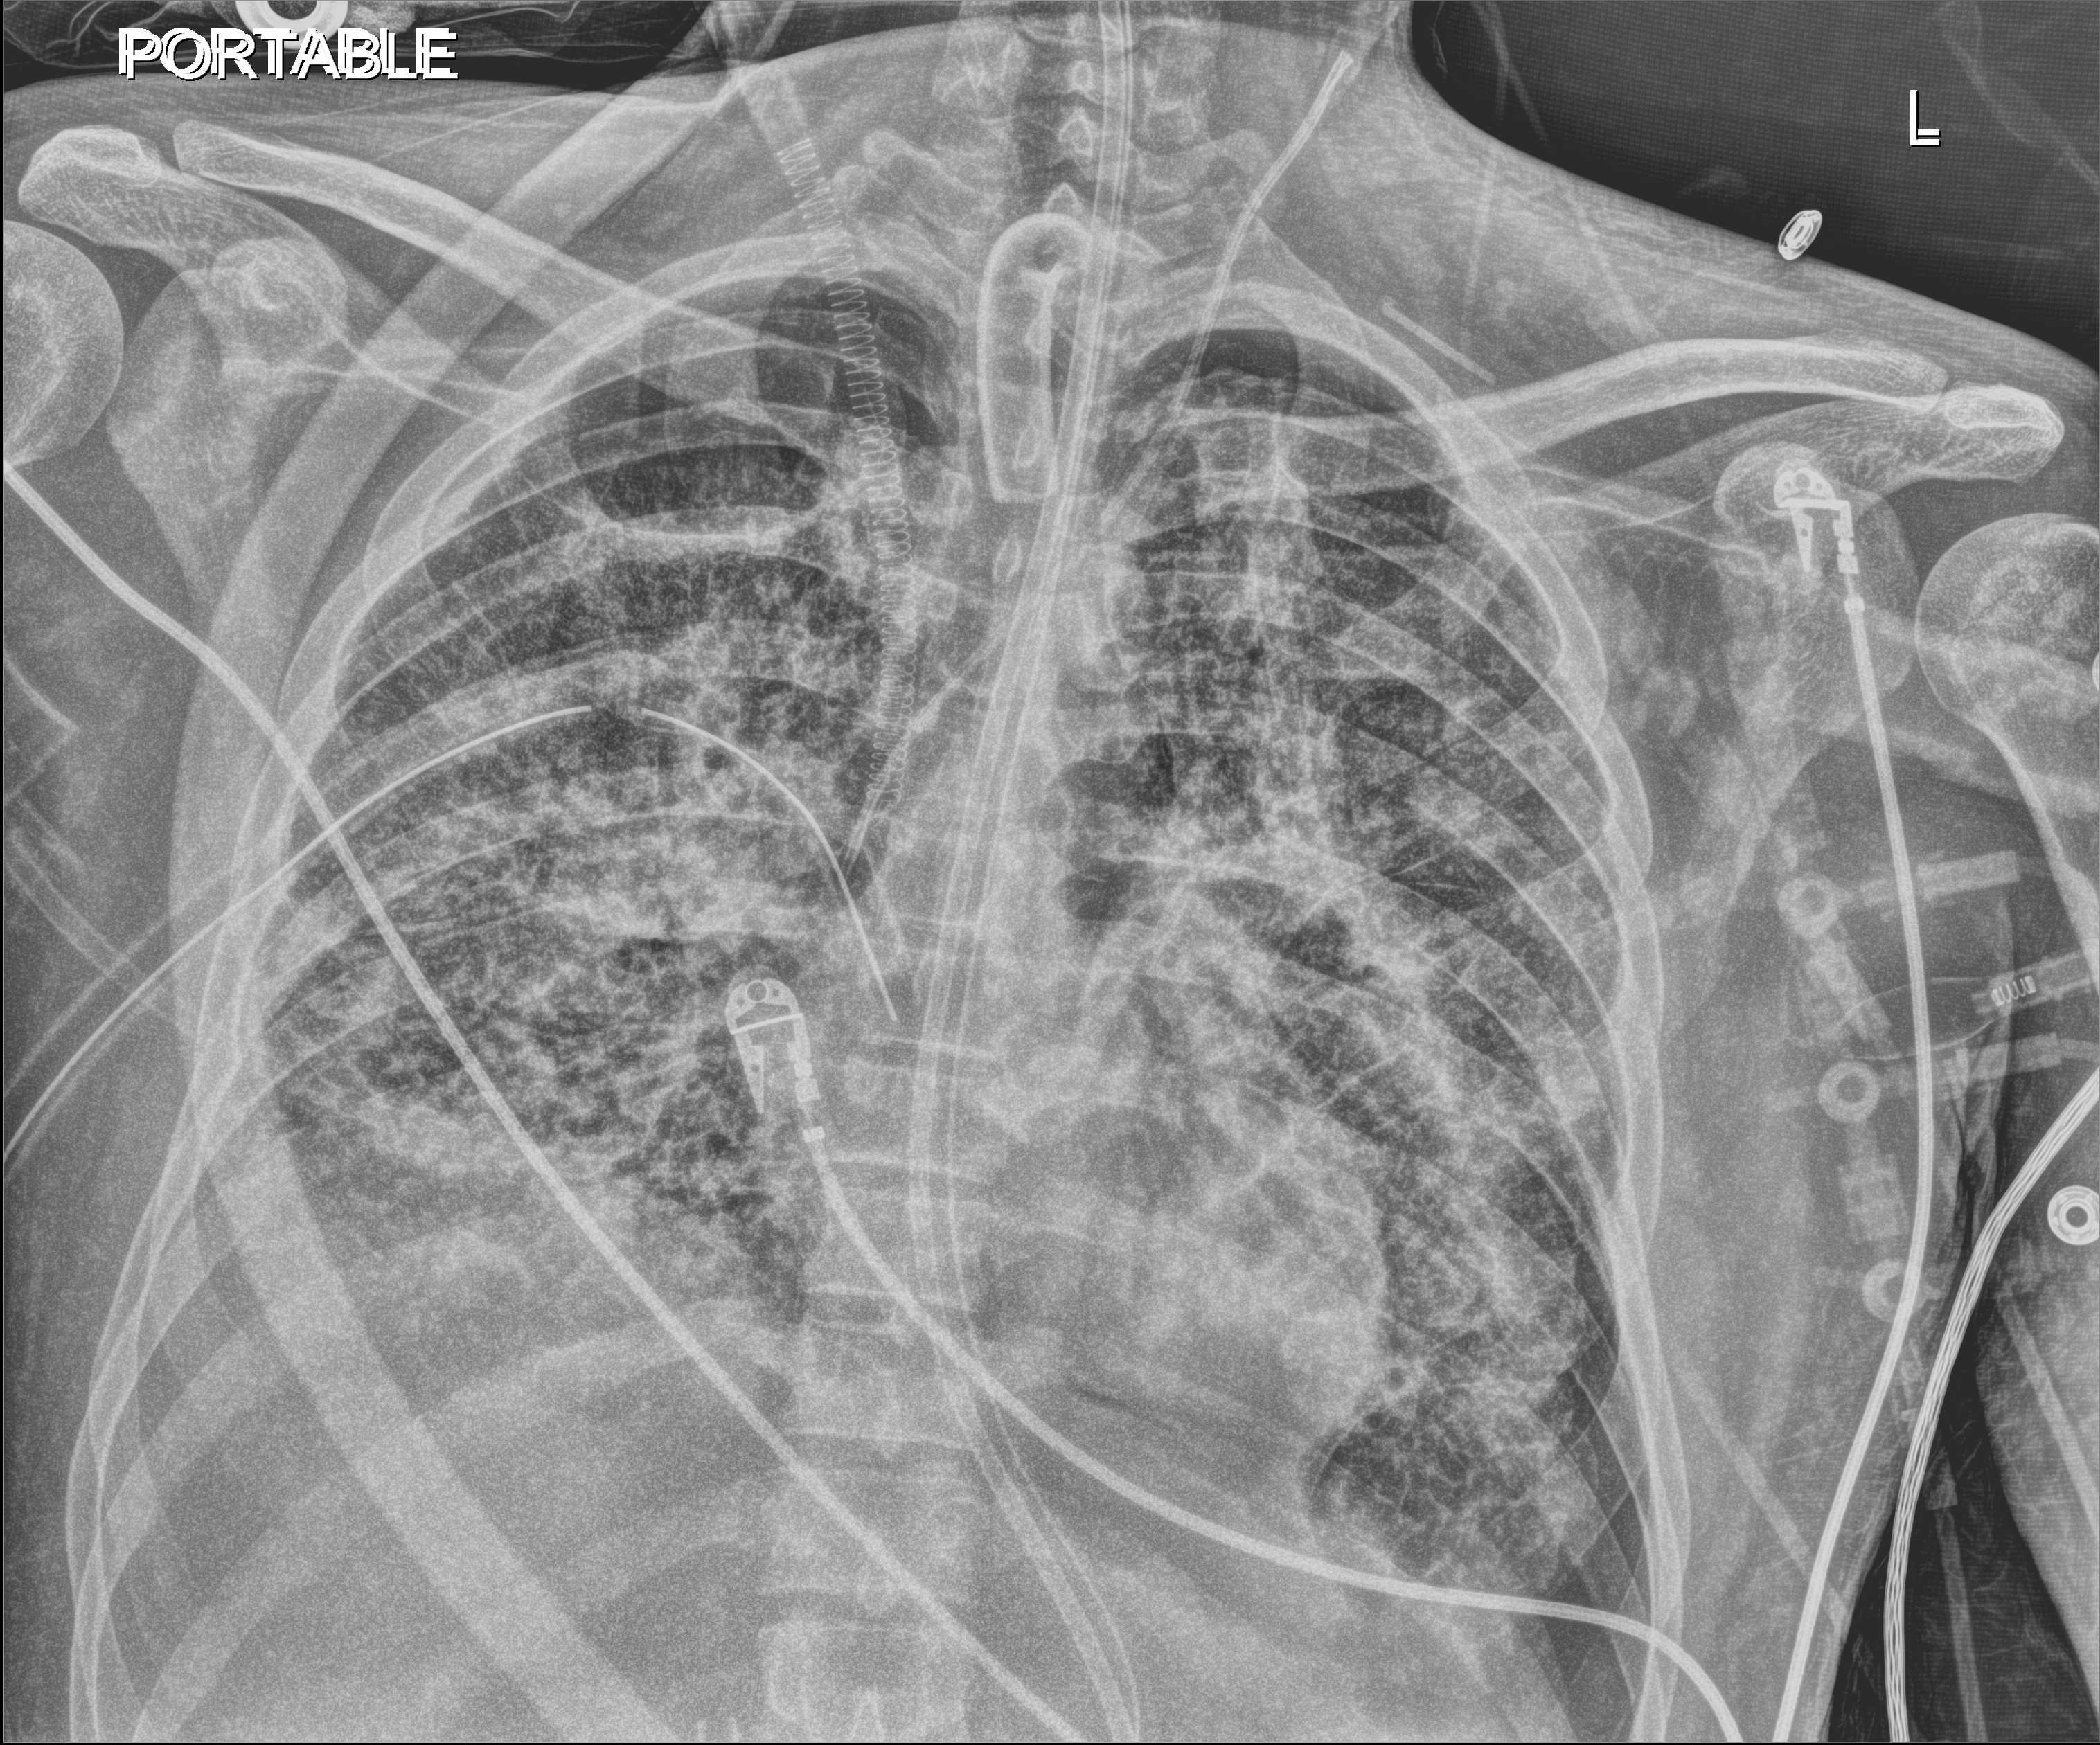
Portable chest radiograph, anteroposterior (AP) projection. Adult patient hospitalised with COVID-19, age 18–59 years.
Hospital-stay facts (about this admission, not read from this image; timing relative to this image not recorded): admitted to intensive care during this hospital stay: yes.